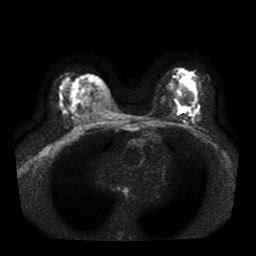
Breast MRI, one axial slice. Slice 22 of 41 in the series (ordered by position). Diffusion-weighted series; image 2 of 4 stored at this slice position (different b-values; order by instance number). 1.5 T. 5 mm slice thickness. 256 × 256 image matrix, field of view 330 × 330 mm. Female patient.
Annotated regions visible in this slice (expert manual segmentation):
- tumour on diffusion-weighted imaging: box from (x=184, y=106) to (x=190, y=110) px